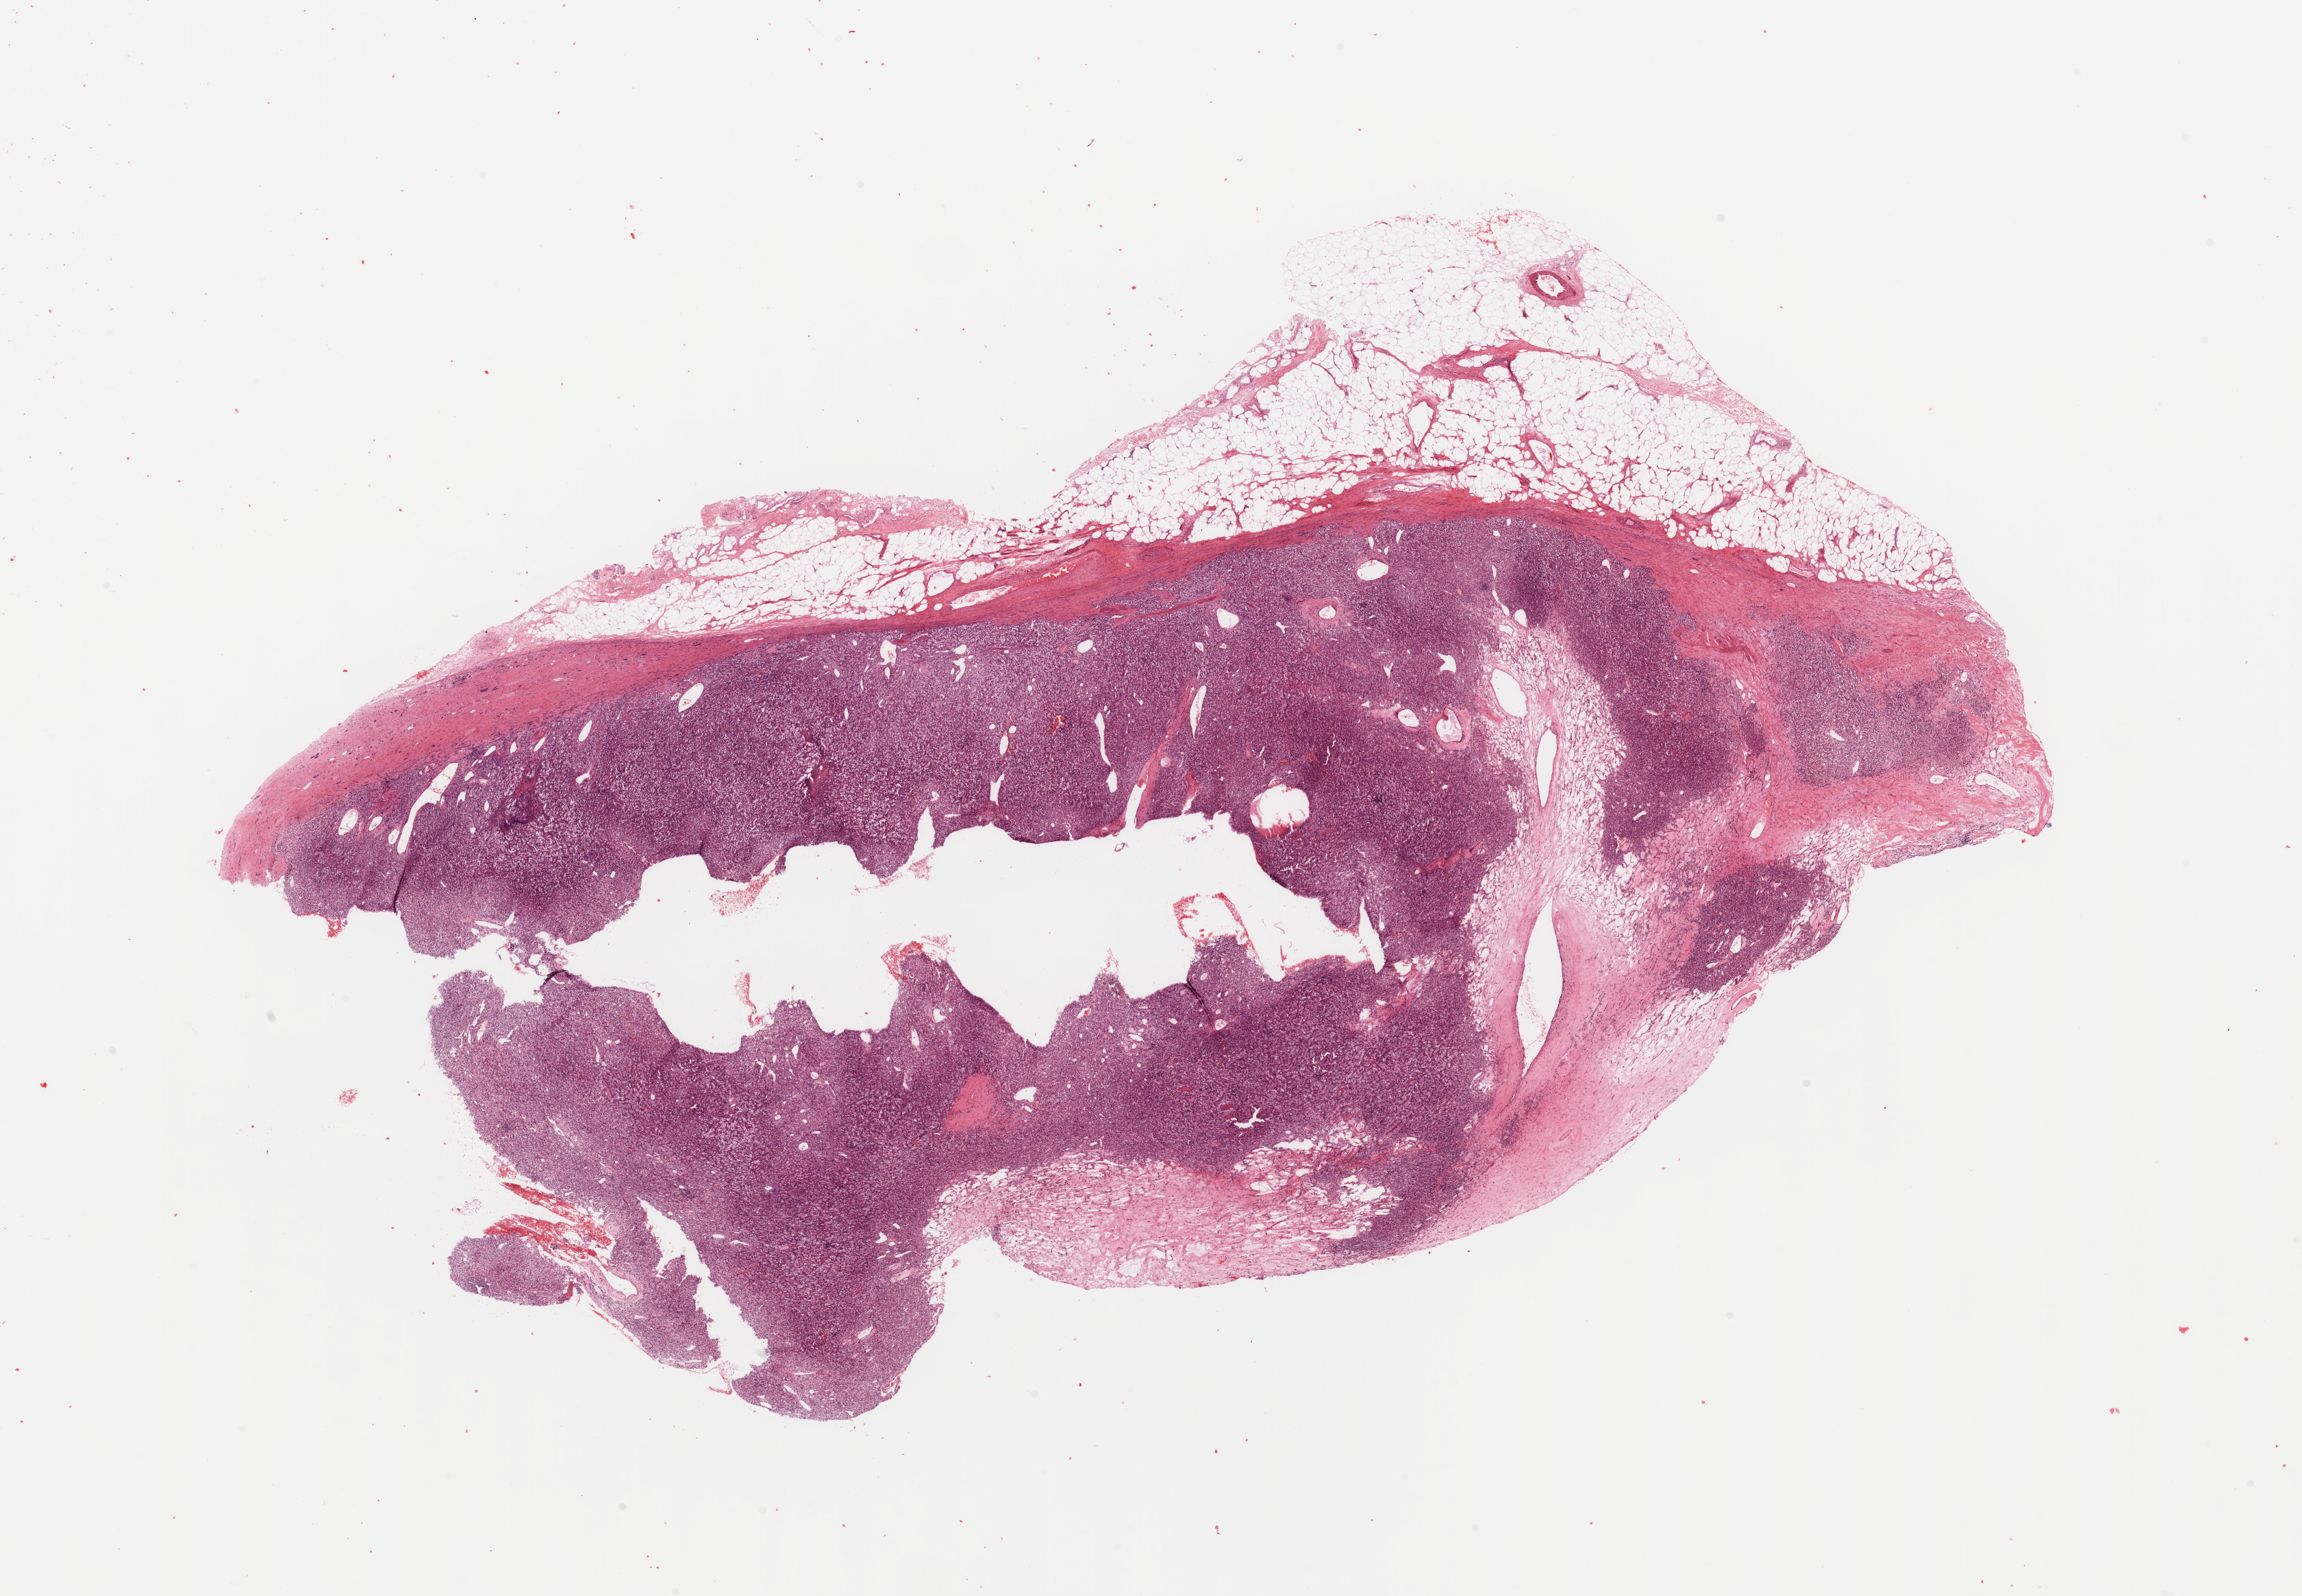
H&E whole-slide image, a low-resolution overview of the entire scanned area, about 26.6 x 18.4 mm (from a 20x scan), kidney, tumour tissue. Male, 63 y/o. Histologic grade: G1 (well differentiated).
• diagnosis: Renal cell carcinoma, NOS